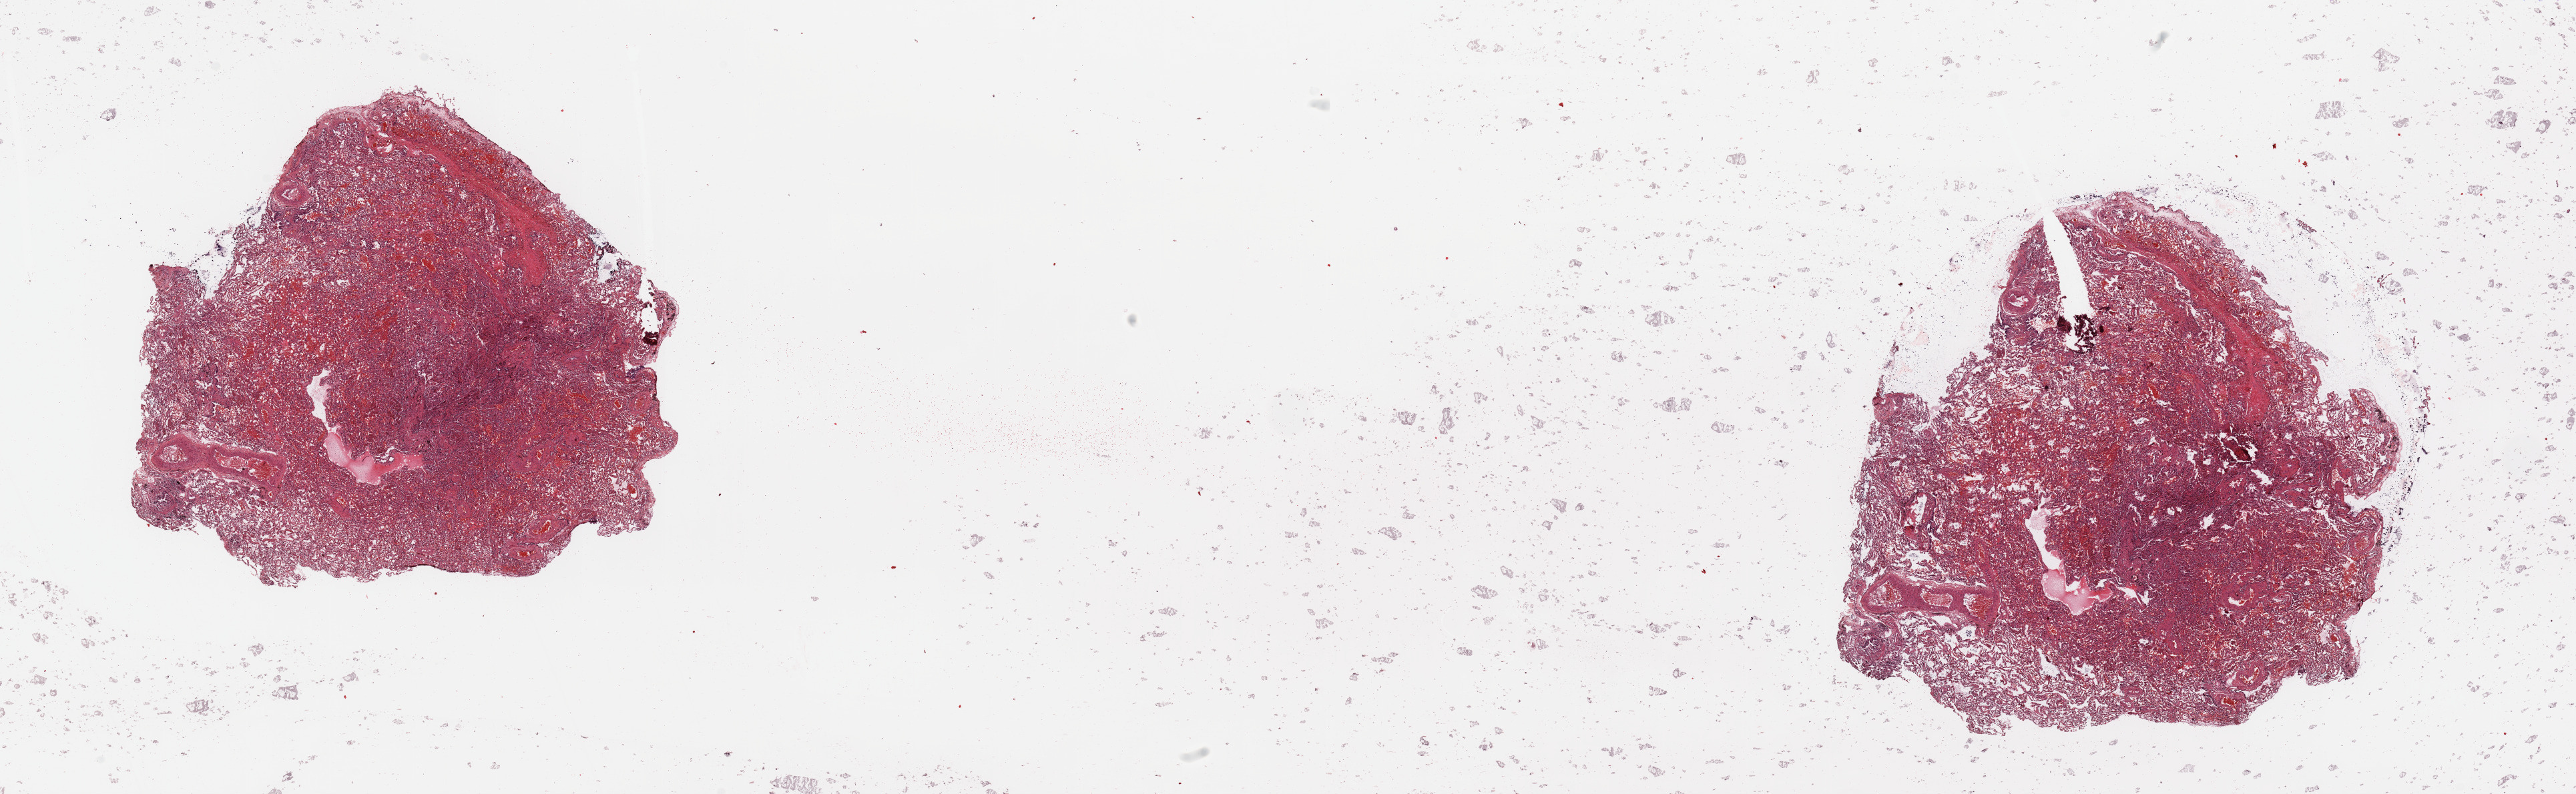
Whole-slide histology image, H&E-stained — low-resolution overview of the scanned area, about 30.5 x 9.4 mm (from a 20x scan), normal (non-tumour) tissue sample, lung. Male, 59 y/o.
This section: normal (non-tumour) tissue from the same patient. Patient diagnosis: Adenocarcinoma, NOS.